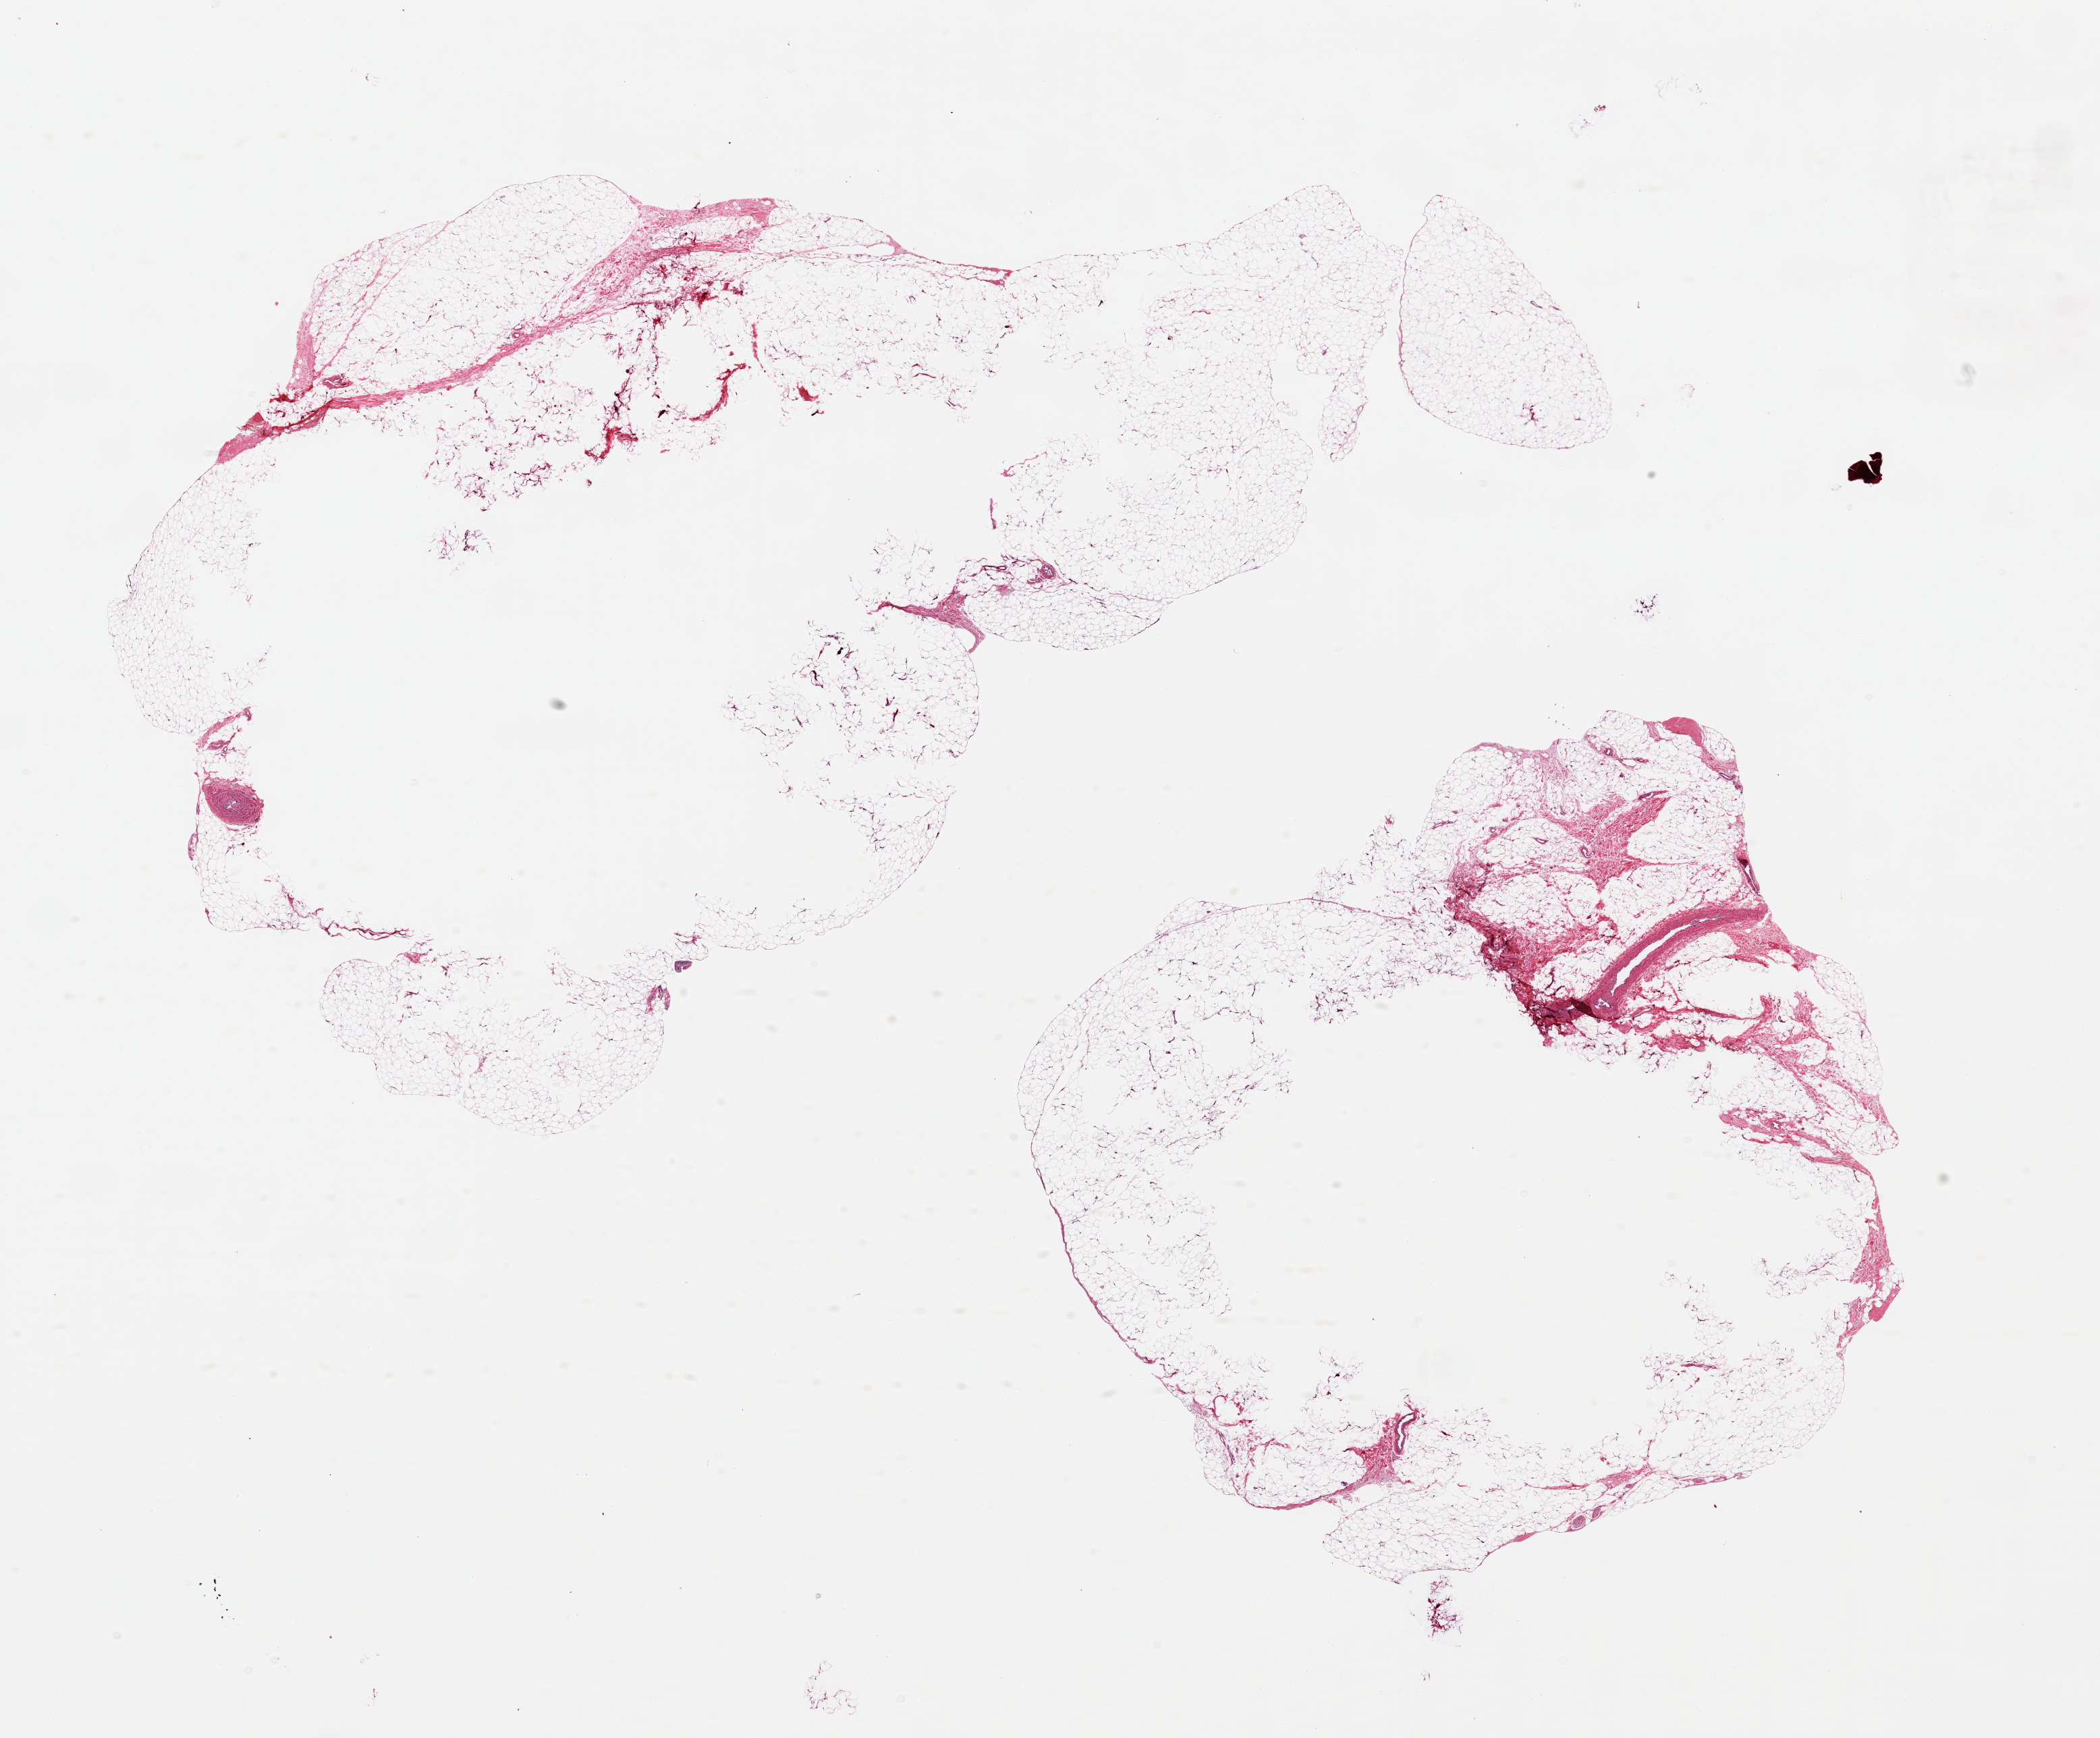
Digitized hematoxylin and eosin (H&E)-stained section, shown as a low-resolution overview of the whole scanned area (about 24.6 x 20.4 mm). PAXgene-fixed paraffin-embedded (PFPE) section. Target tissue: adipose tissue. Tissue donor sample. Donor sex: female.
Pathologist's review note for this sample: 2 pieces 16x9 & 9x8 mm; large central hollow defects in each piece, probably poorly fixed.